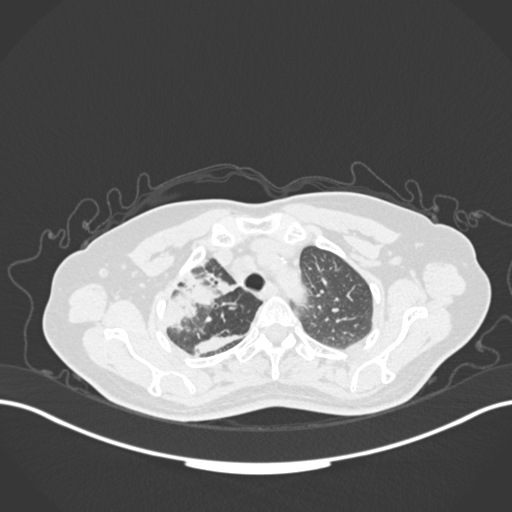
Chest CT, one axial slice. Slice 131 of 177 in the series (ordered by position). Reconstruction kernel B30f. Lung window (W 1500 / L -600 HU). 1 mm slice thickness. 512 × 512 image matrix, field of view 400 × 400 mm. Female patient, age 60 years. From the clinical record (not read from this slice): clinical TNM (as recorded): T3 N1 M1.
Annotated regions visible in this slice (bounding box drawn by a radiologist):
- lung tumour (recorded histology: adenocarcinoma): bounding box <162,261,242,335> (left, top, right, bottom; pixels)